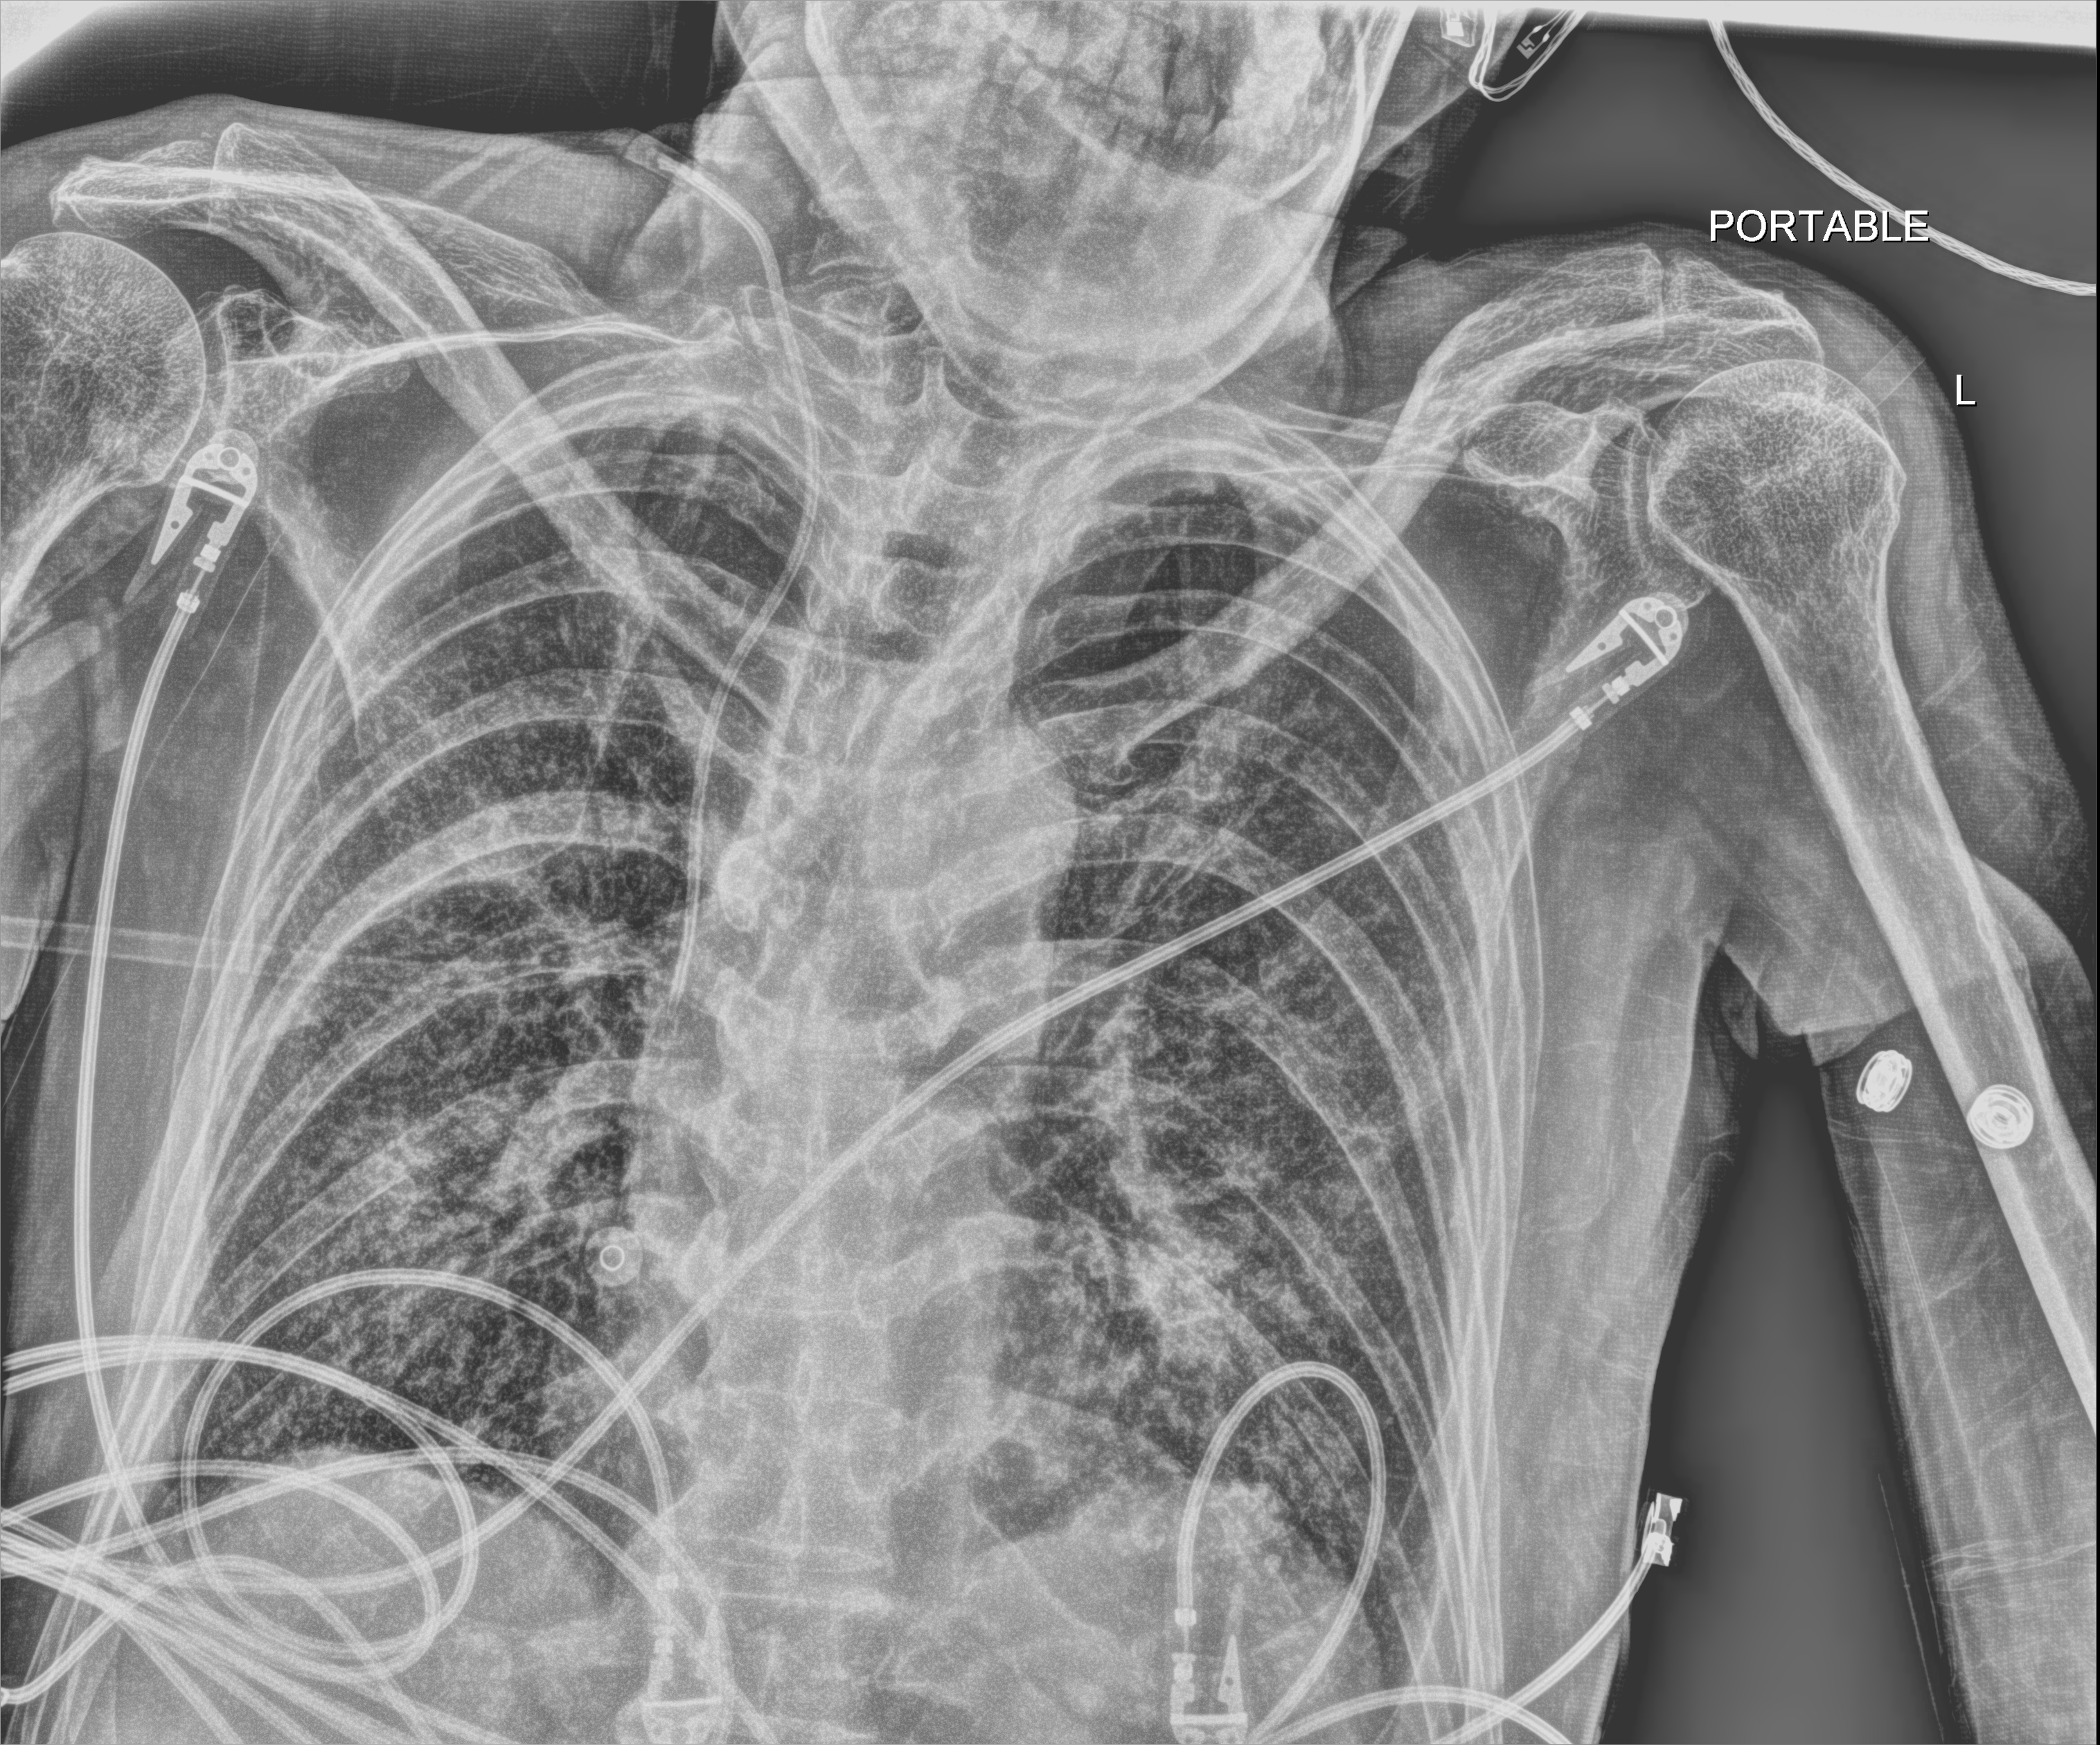
Bedside chest radiograph (digital radiography); anteroposterior (AP) projection. Patient hospitalised with COVID-19; male, aged 60–74 years.
Admission-level facts for this patient (not findings on this image; timing relative to this image not recorded): admitted to intensive care during this hospital stay: yes.